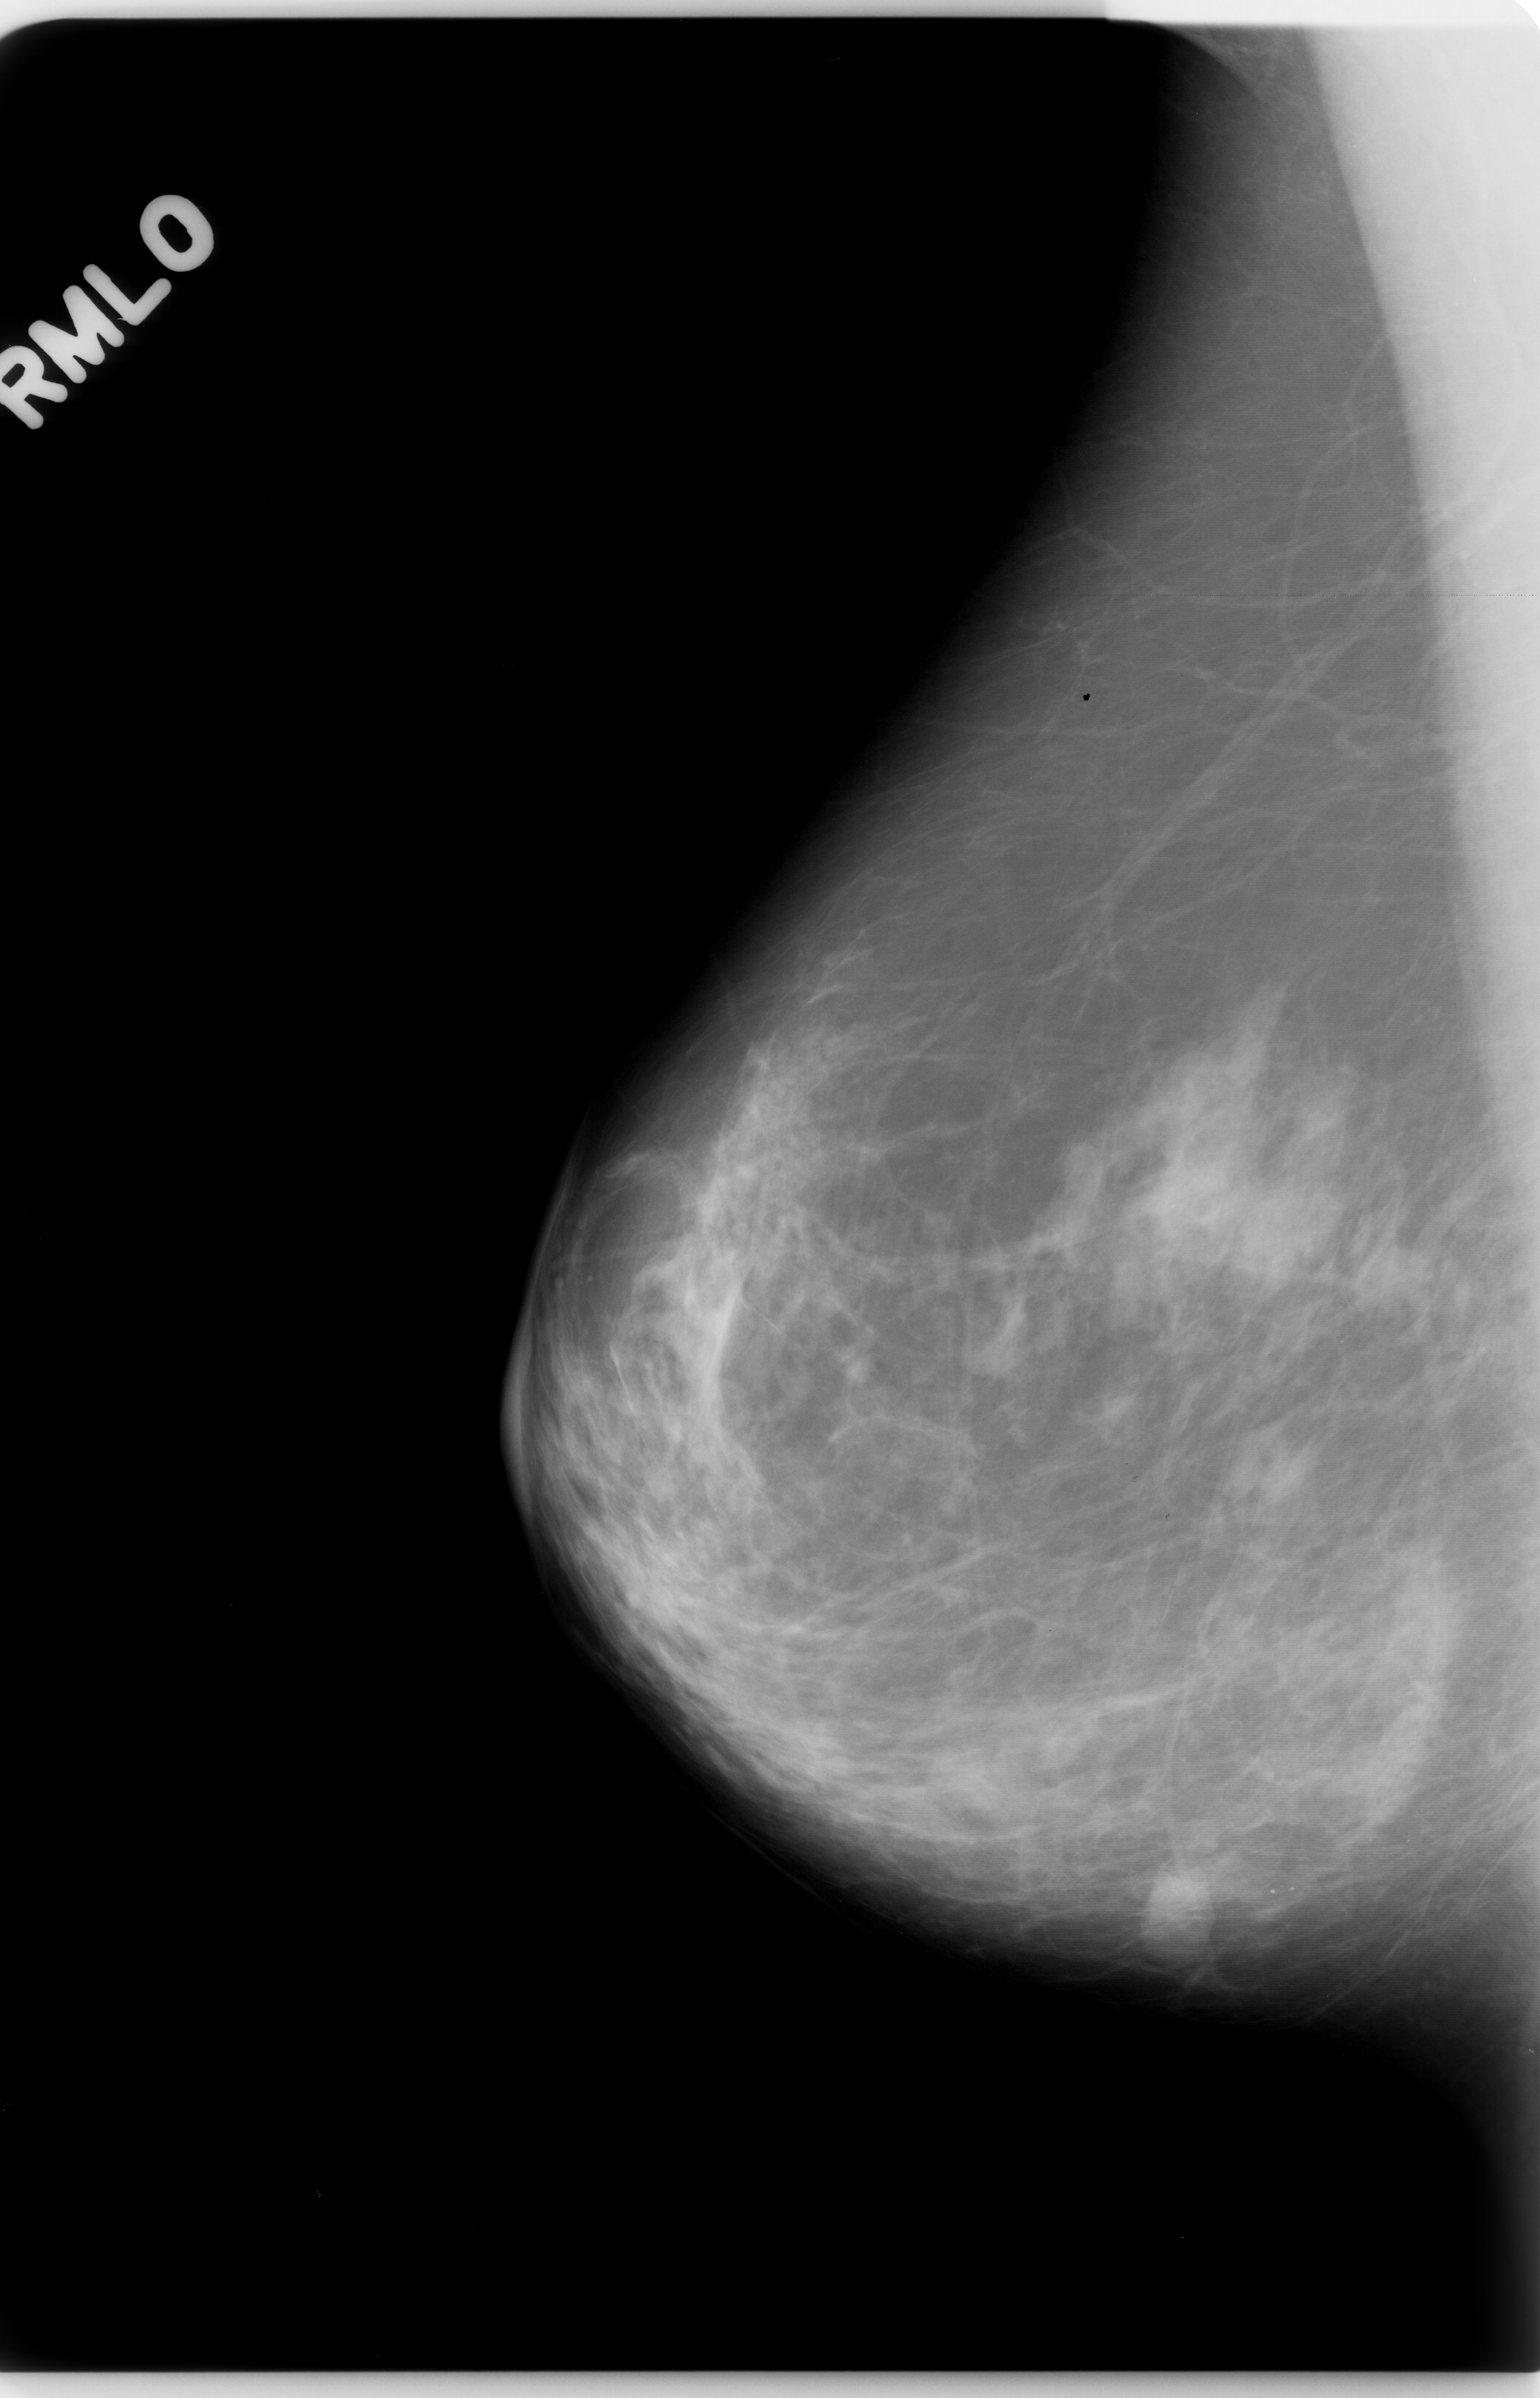
Mammogram (digitized film); right breast; mediolateral oblique (MLO) view; breast composition: scattered fibroglandular densities (BI-RADS density category 2 of 4); 1540 × 2398 image matrix.
Expert-marked regions of interest on this film, with their recorded descriptors:
- mass, shape oval, margins circumscribed; BI-RADS assessment category 4; pathology (as recorded): benign: bounding box (x1, y1, x2, y2) in pixels: (1130, 1853, 1221, 1949)